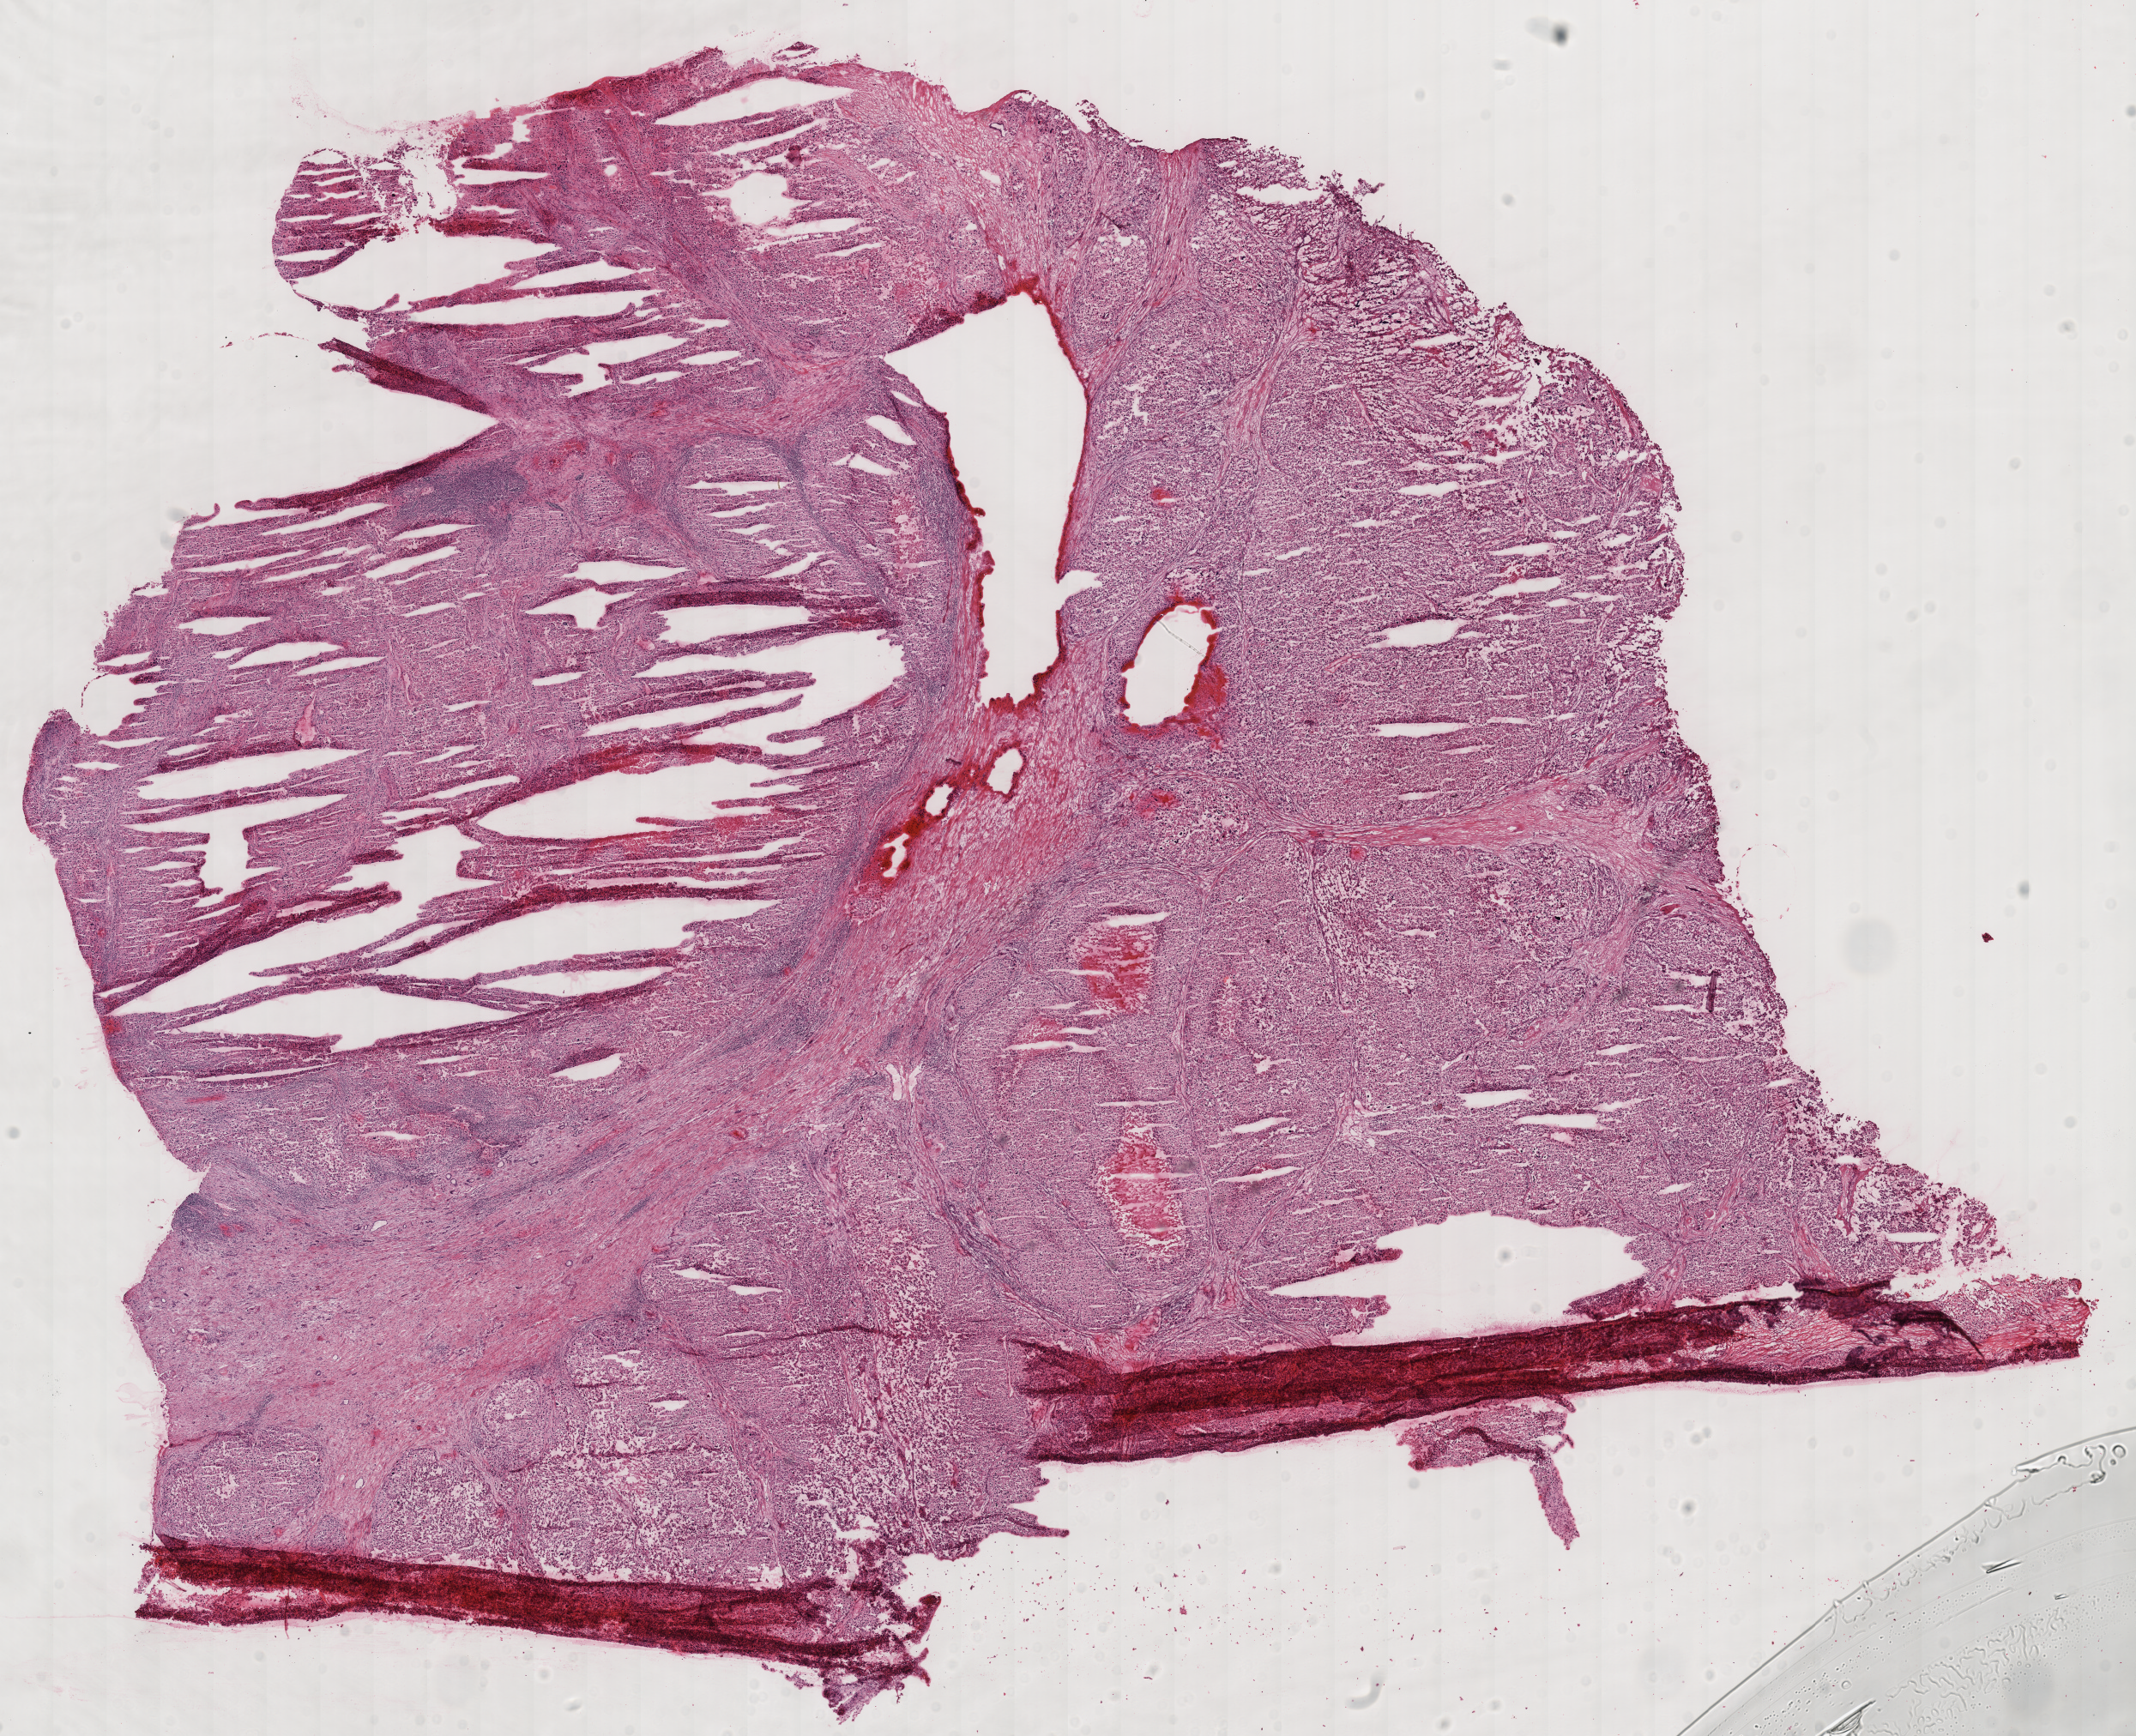
Digitized Hematoxylin and eosin (H&E) stained tissue section (whole slide) — a low-resolution overview of the entire scanned area, about 19.6 x 15.9 mm (from a 40x scan), frozen section from the top of the tissue portion, kidney, primary tumour sample. Patient: male, age at initial diagnosis 71 years. Composition of this section per pathologist review: tumour cells 85%, tumour nuclei 85%, normal cells 0%, stromal cells 10%, necrosis 5%. Inflammatory infiltration, as recorded: lymphocyte infiltration 10%, monocyte infiltration 0%, neutrophil infiltration 0%.
AJCC pathologic stage: II. Histologic diagnosis: Renal cell carcinoma, chromophobe type. Lymph nodes positive (case pathology): 0 of 1 examined. Laterality: left.